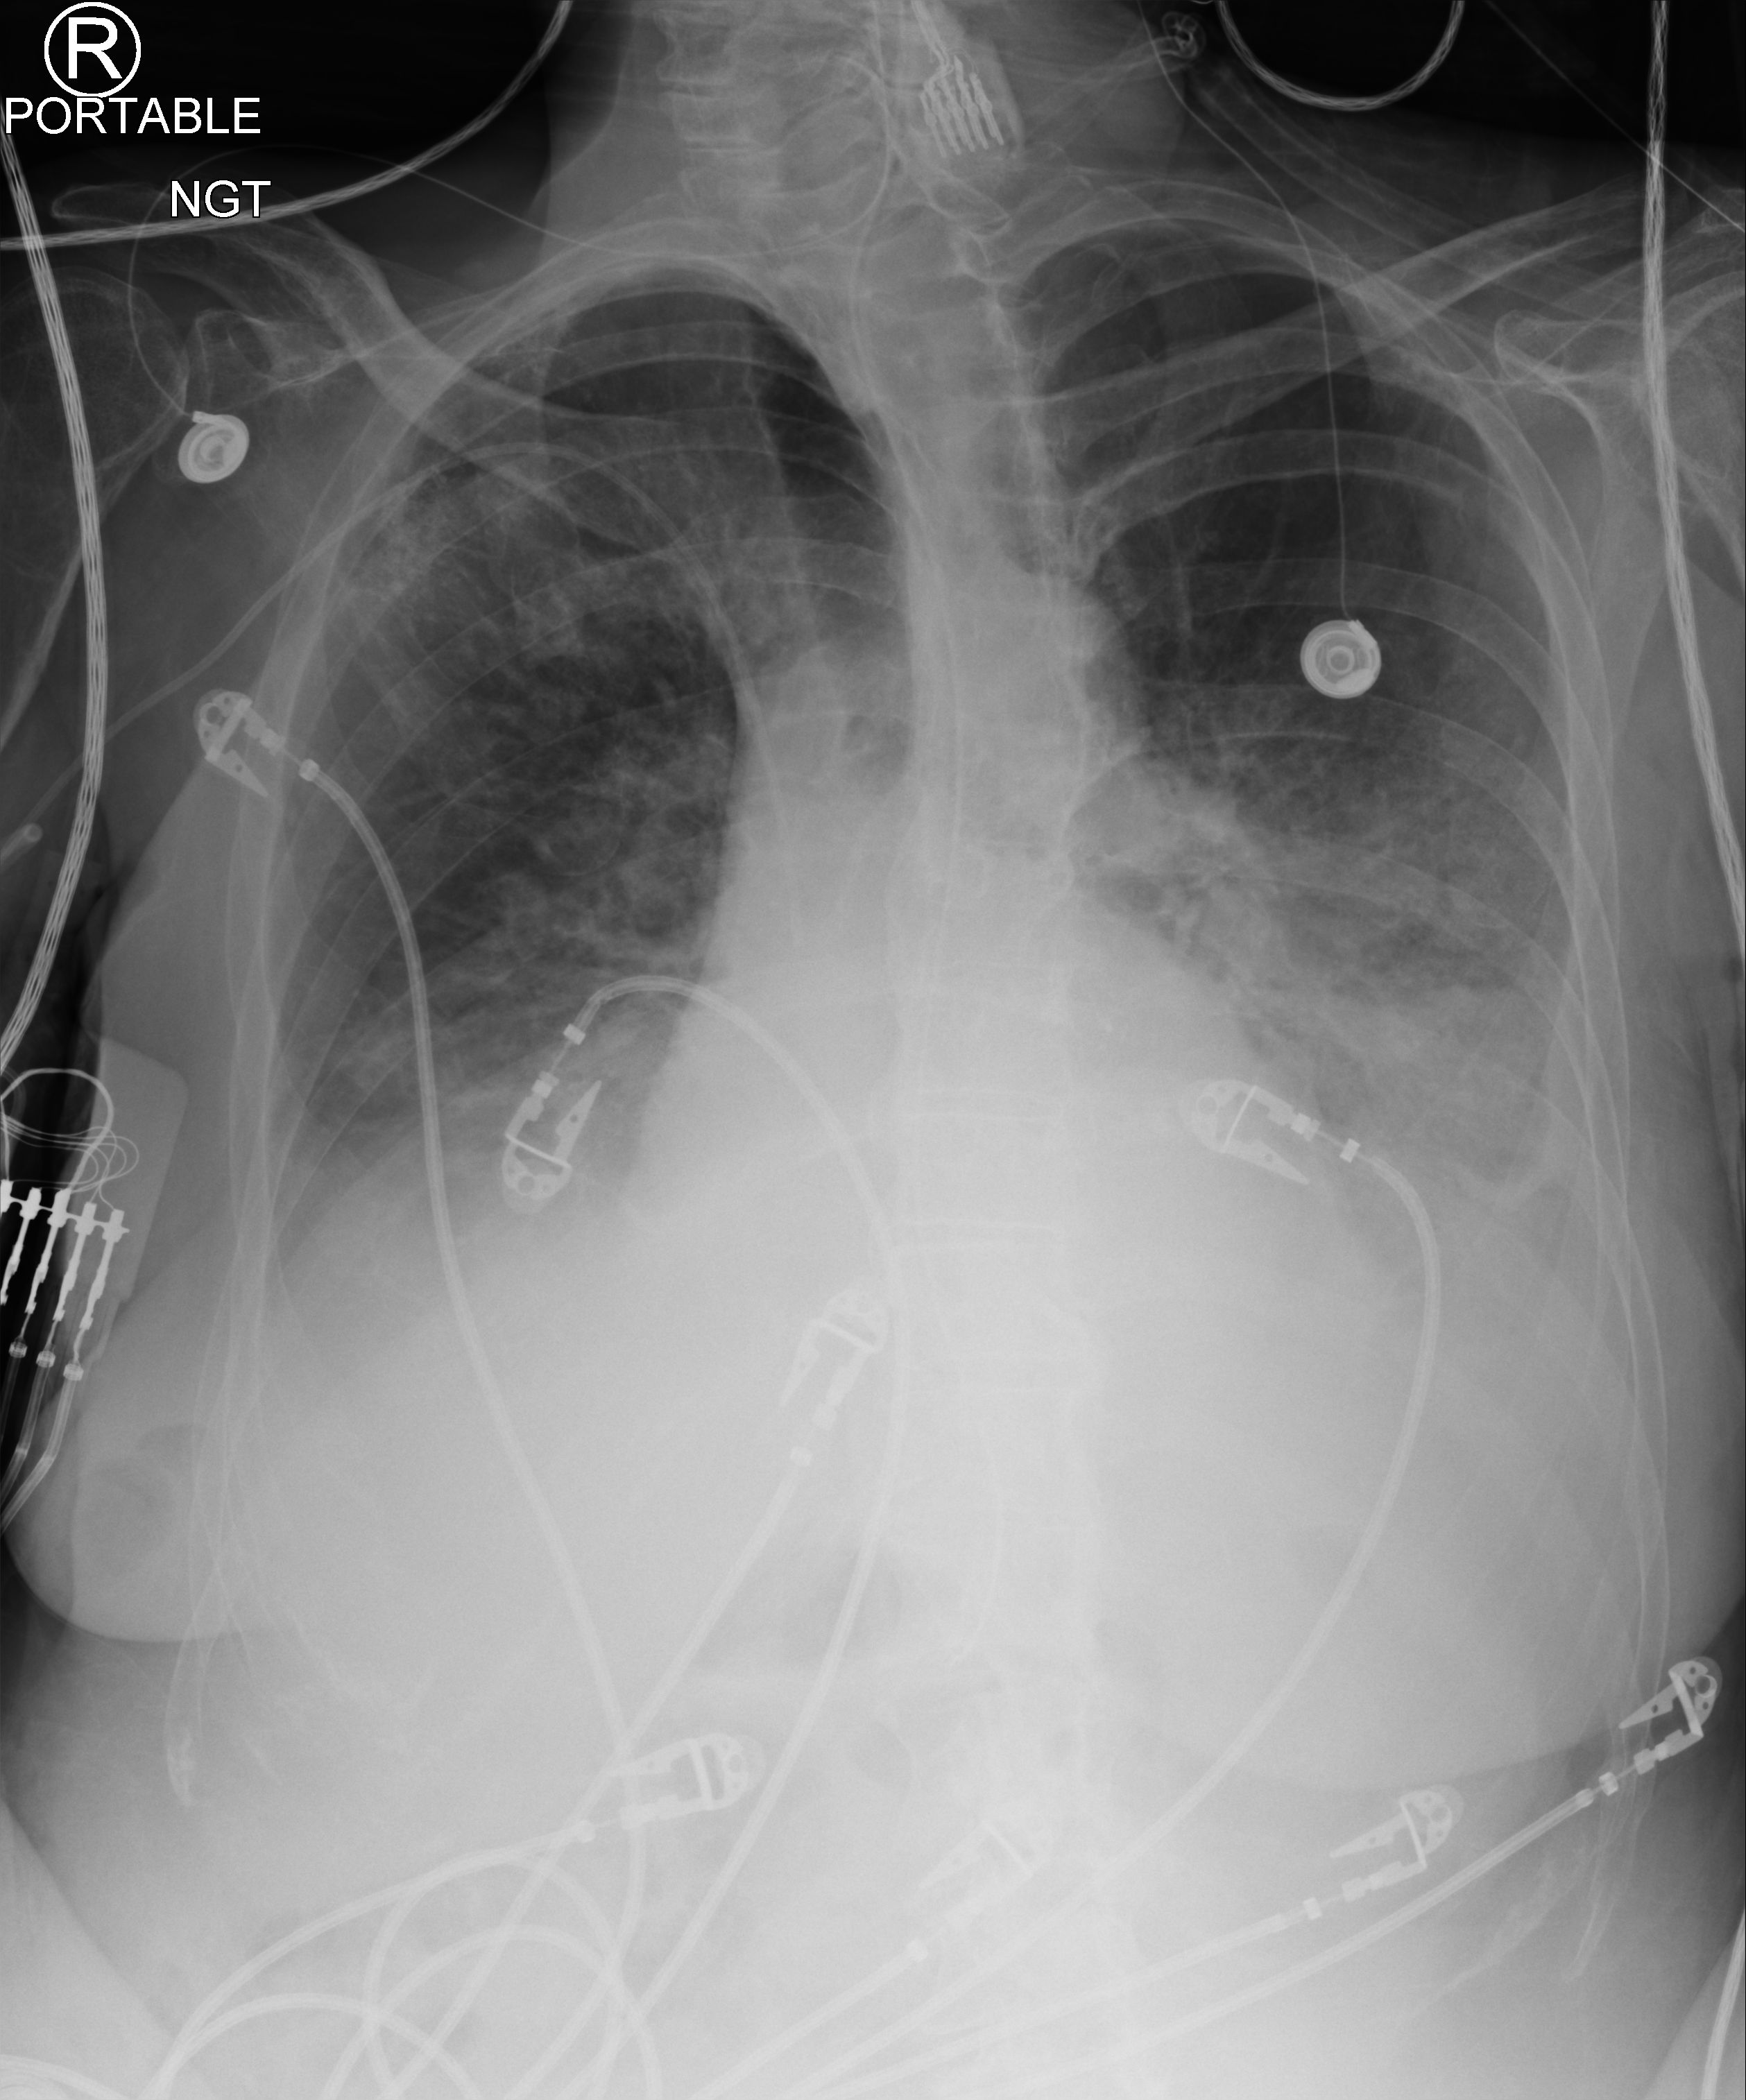
Portable chest radiograph; anteroposterior (AP) projection. Female patient hospitalised with COVID-19, age 60–74 years.
Admission-level facts for this patient (not findings on this image; timing relative to this image not recorded):
- length of hospital stay: 10 days
- admitted to intensive care during this hospital stay: yes
- mechanically ventilated during this hospital stay: no